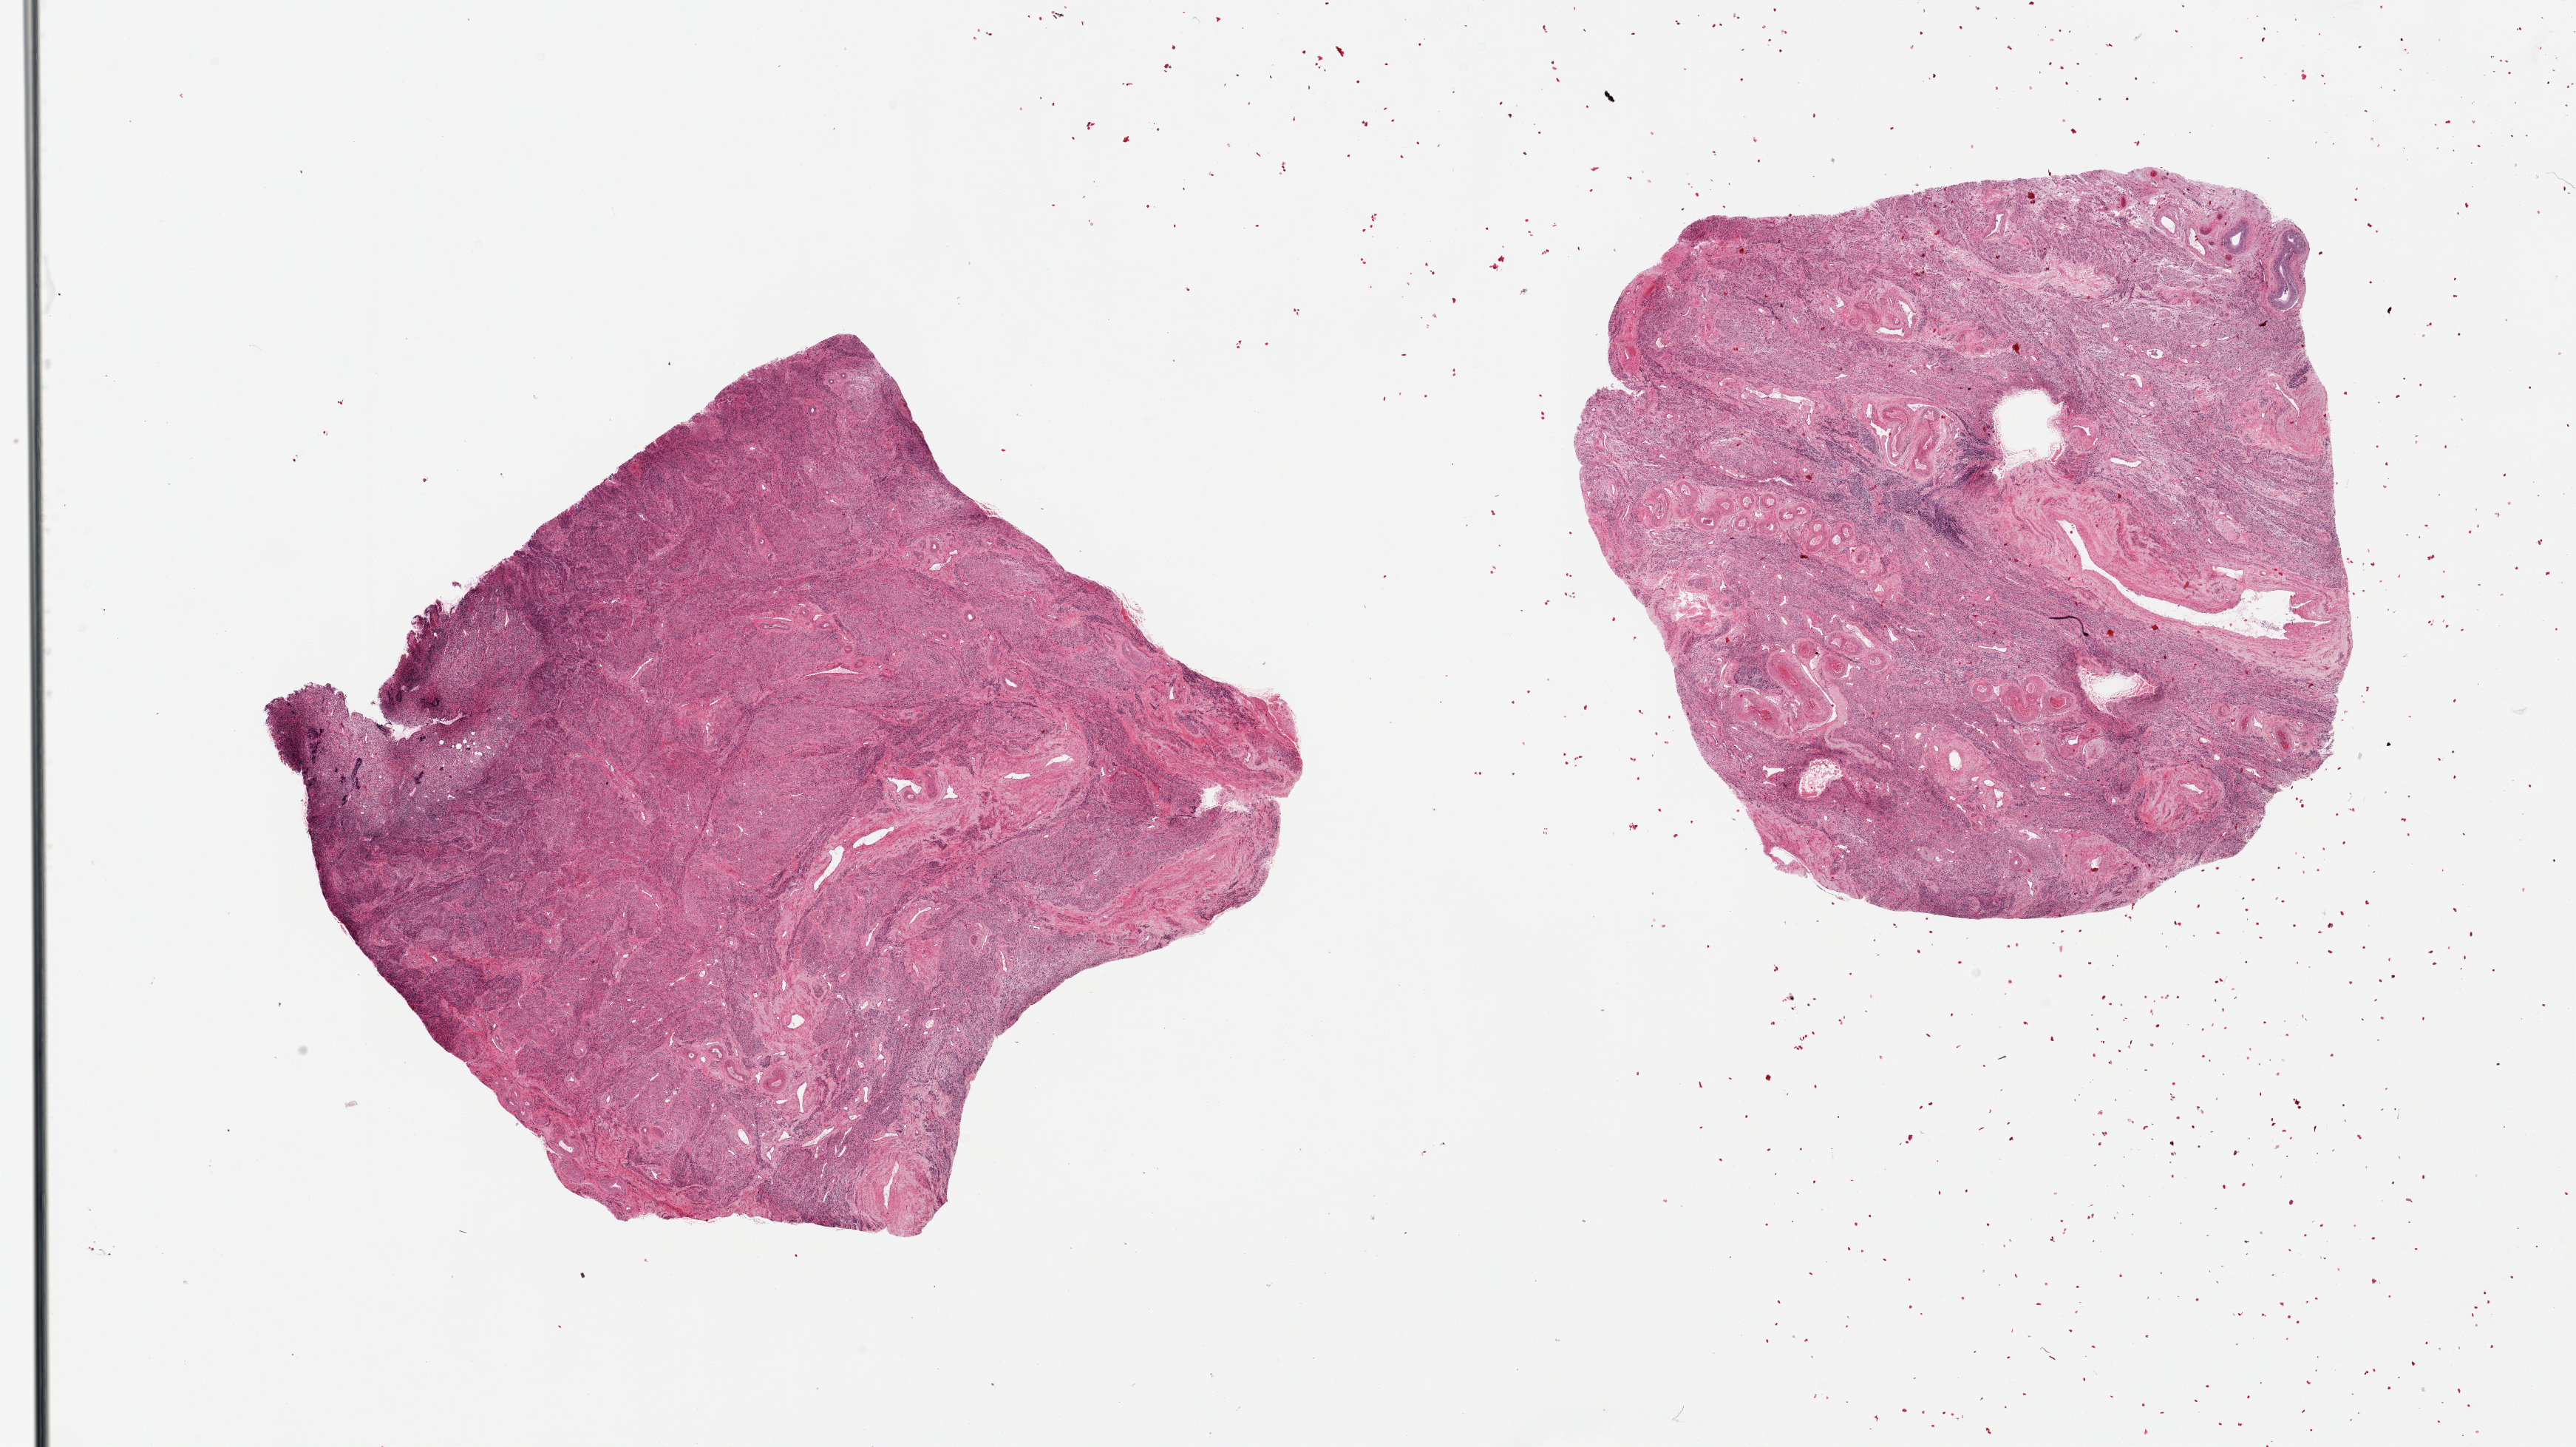
Haematoxylin and eosin whole-slide image — a low-resolution overview of the entire scanned area, about 27.6 x 15.5 mm (from a 20x scan), PAXgene-fixed, paraffin-embedded tissue, sampled site (target tissue): uterus, tissue donor sample. Female donor.
- pathologist's review note for this sample: 2 pieces, mainly myometrium, focal autolyzed stroma